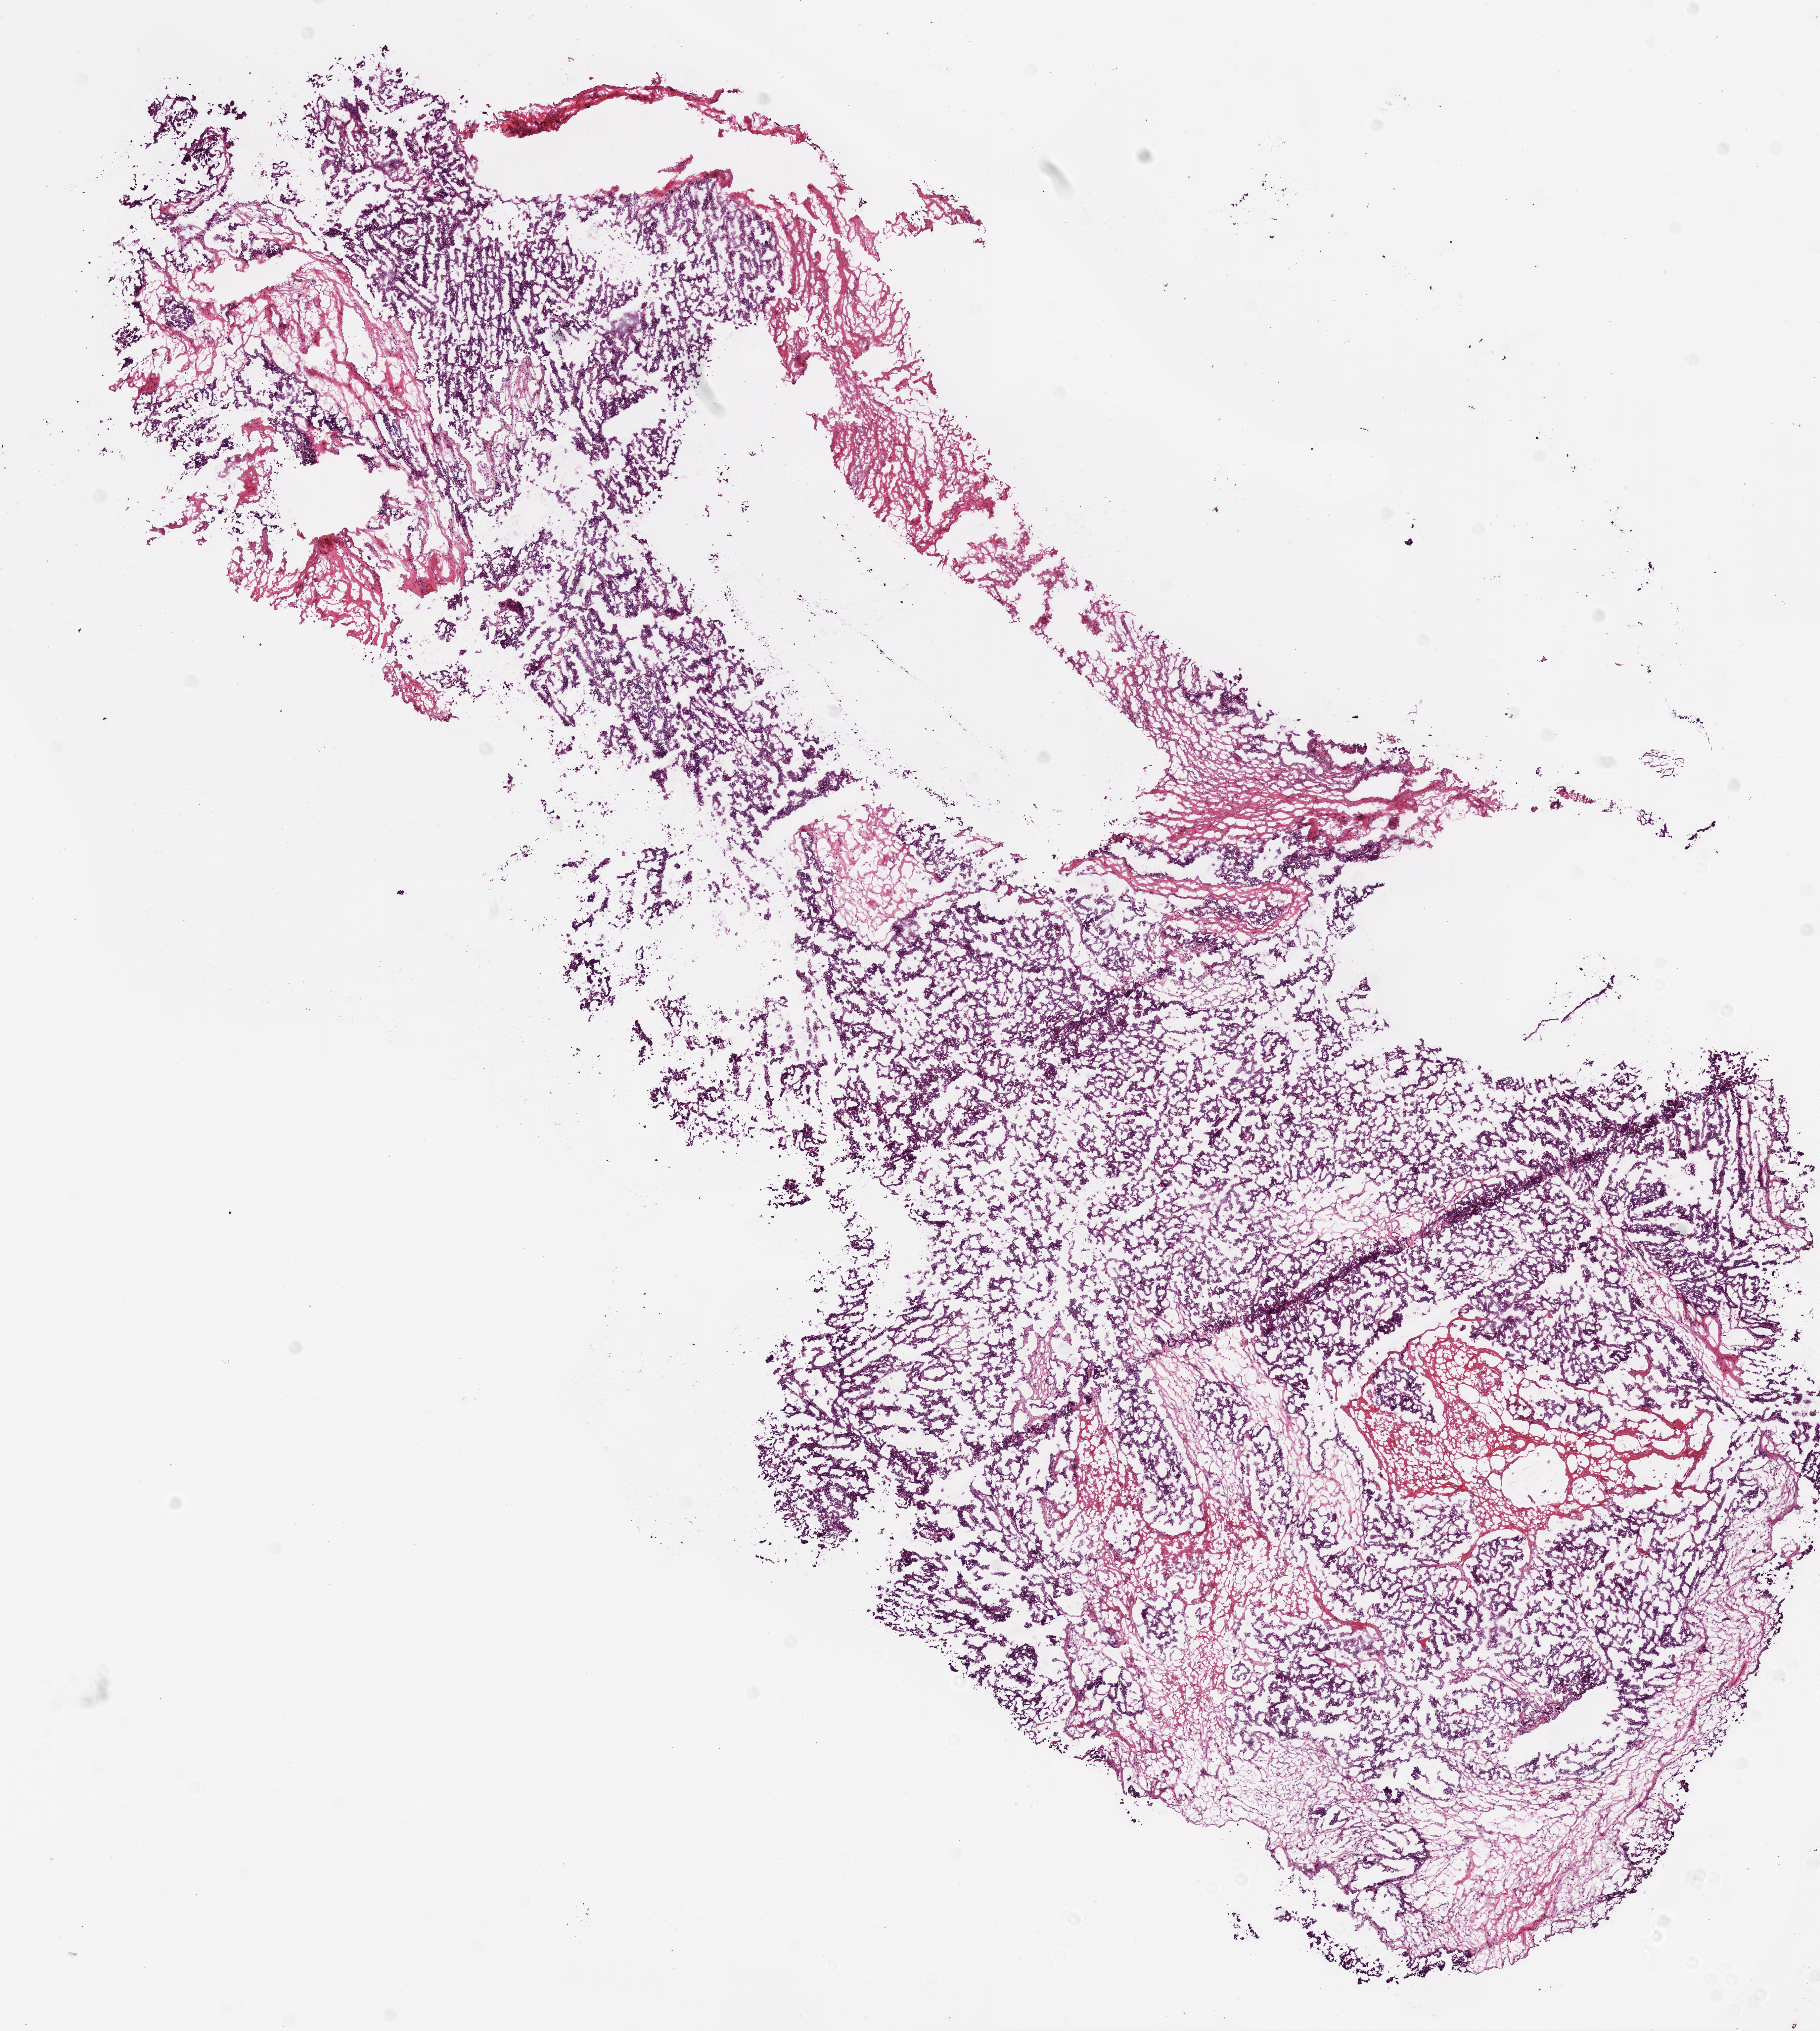
H&E-stained whole-slide image, low-resolution overview of the scanned area, about 11.0 x 12.3 mm (acquisition: 20x scan); frozen section; ovary, primary tumour sample. Patient: female, age at initial diagnosis 73 years.
Histologic diagnosis: Serous cystadenocarcinoma, NOS.